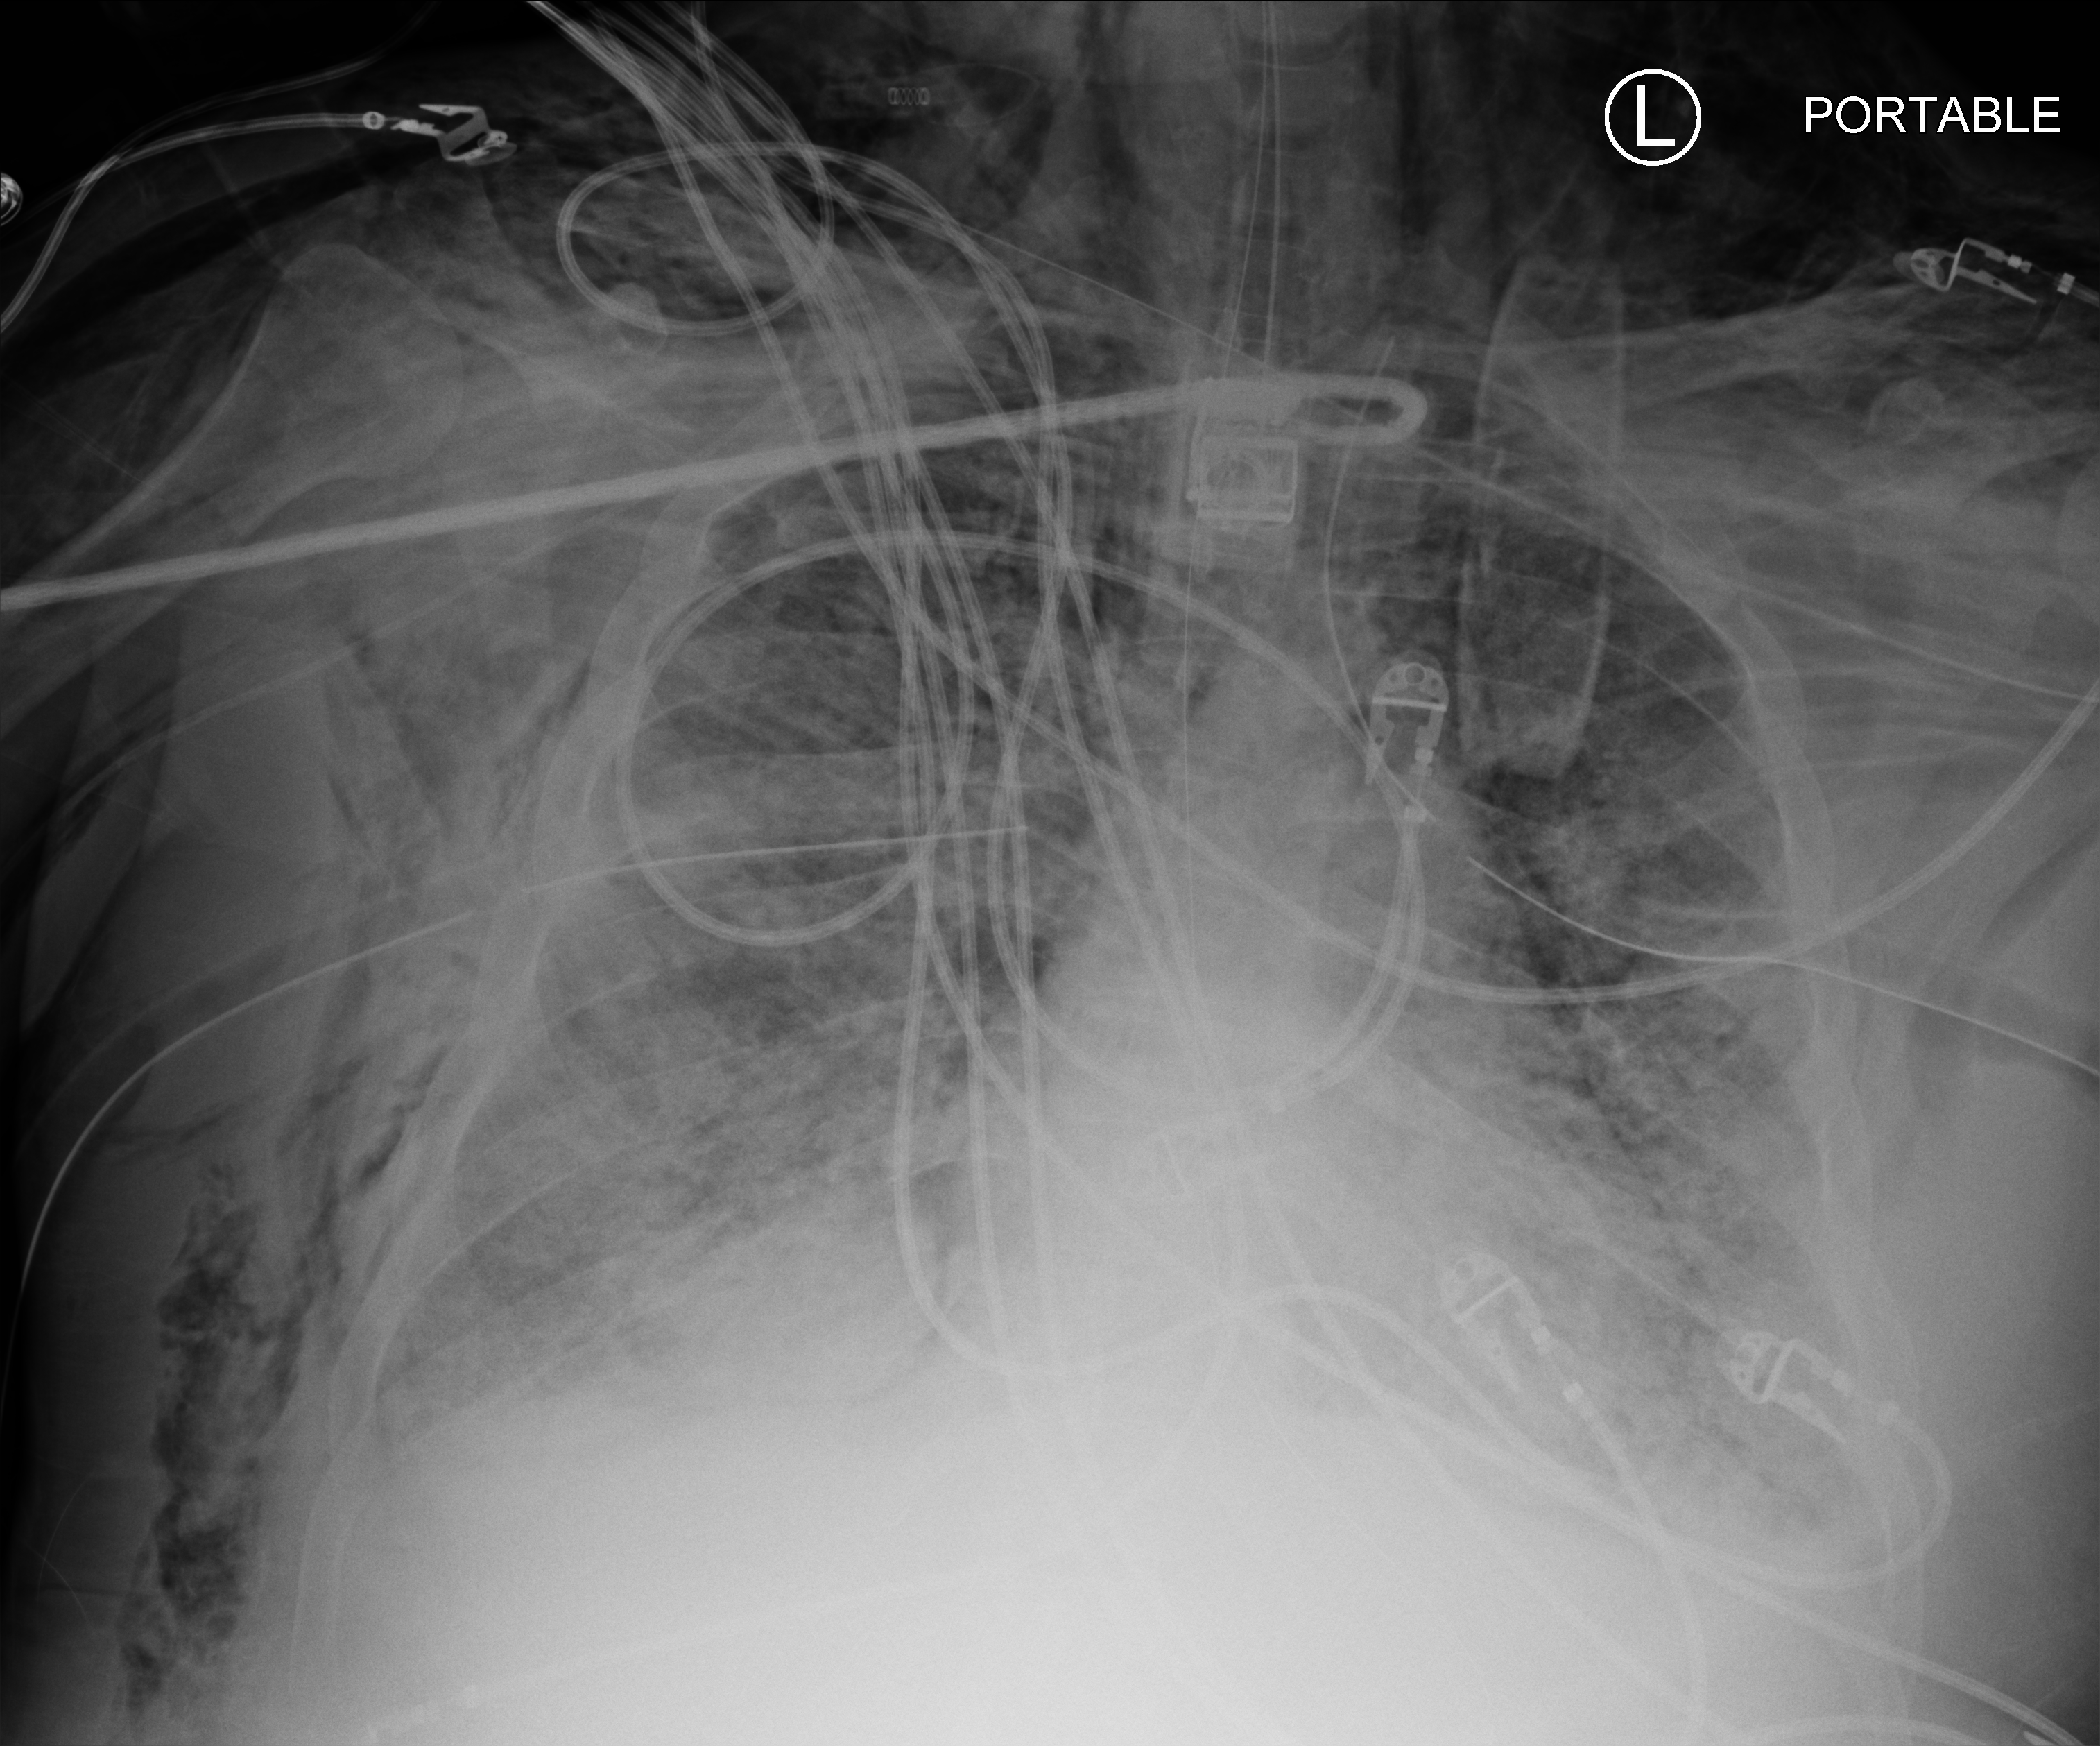
Portable chest radiograph. Patient hospitalised with COVID-19, aged 18–59 years.
Hospital-stay facts (about this admission, not read from this image; timing relative to this image not recorded):
- admitted to intensive care during this hospital stay: yes
- mechanically ventilated during this hospital stay: yes
- diabetes (admission record): no